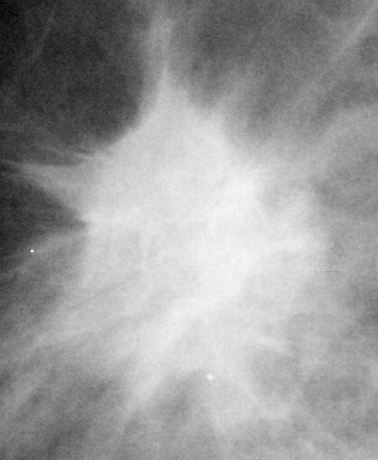
Crop from a digitized film mammogram around one marked abnormality; right breast; MLO view.
- Finding: mass, shape irregular, margins spiculated; BI-RADS assessment category 5; pathology result (as recorded, not read from the image): malignant.